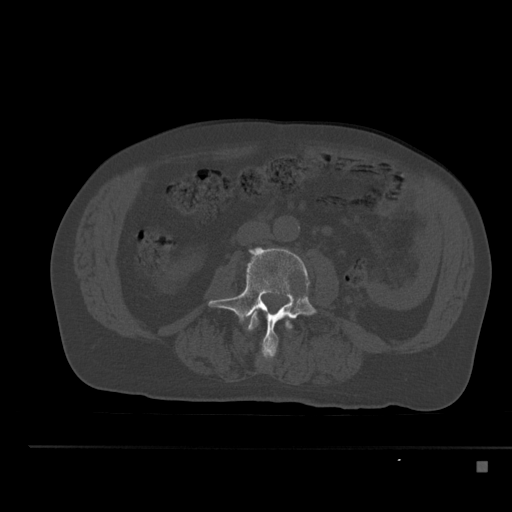
CT including the spine, one axial slice; slice 166 of 517 in the series (ordered by position); 120 kVp; bone window (W 1800 / L 400 HU); 512 × 512 image matrix. Male patient, age 70 years. Case-level facts recorded for this patient, not image findings: primary cancer: renal.
Outlined on this slice (semi-automatic segmentation, software-assisted and operator-edited):
- L2 vertebra: bounding box [x1, y1, x2, y2] px = [246, 311, 293, 356]
- L3 vertebra: [208, 247, 317, 361]